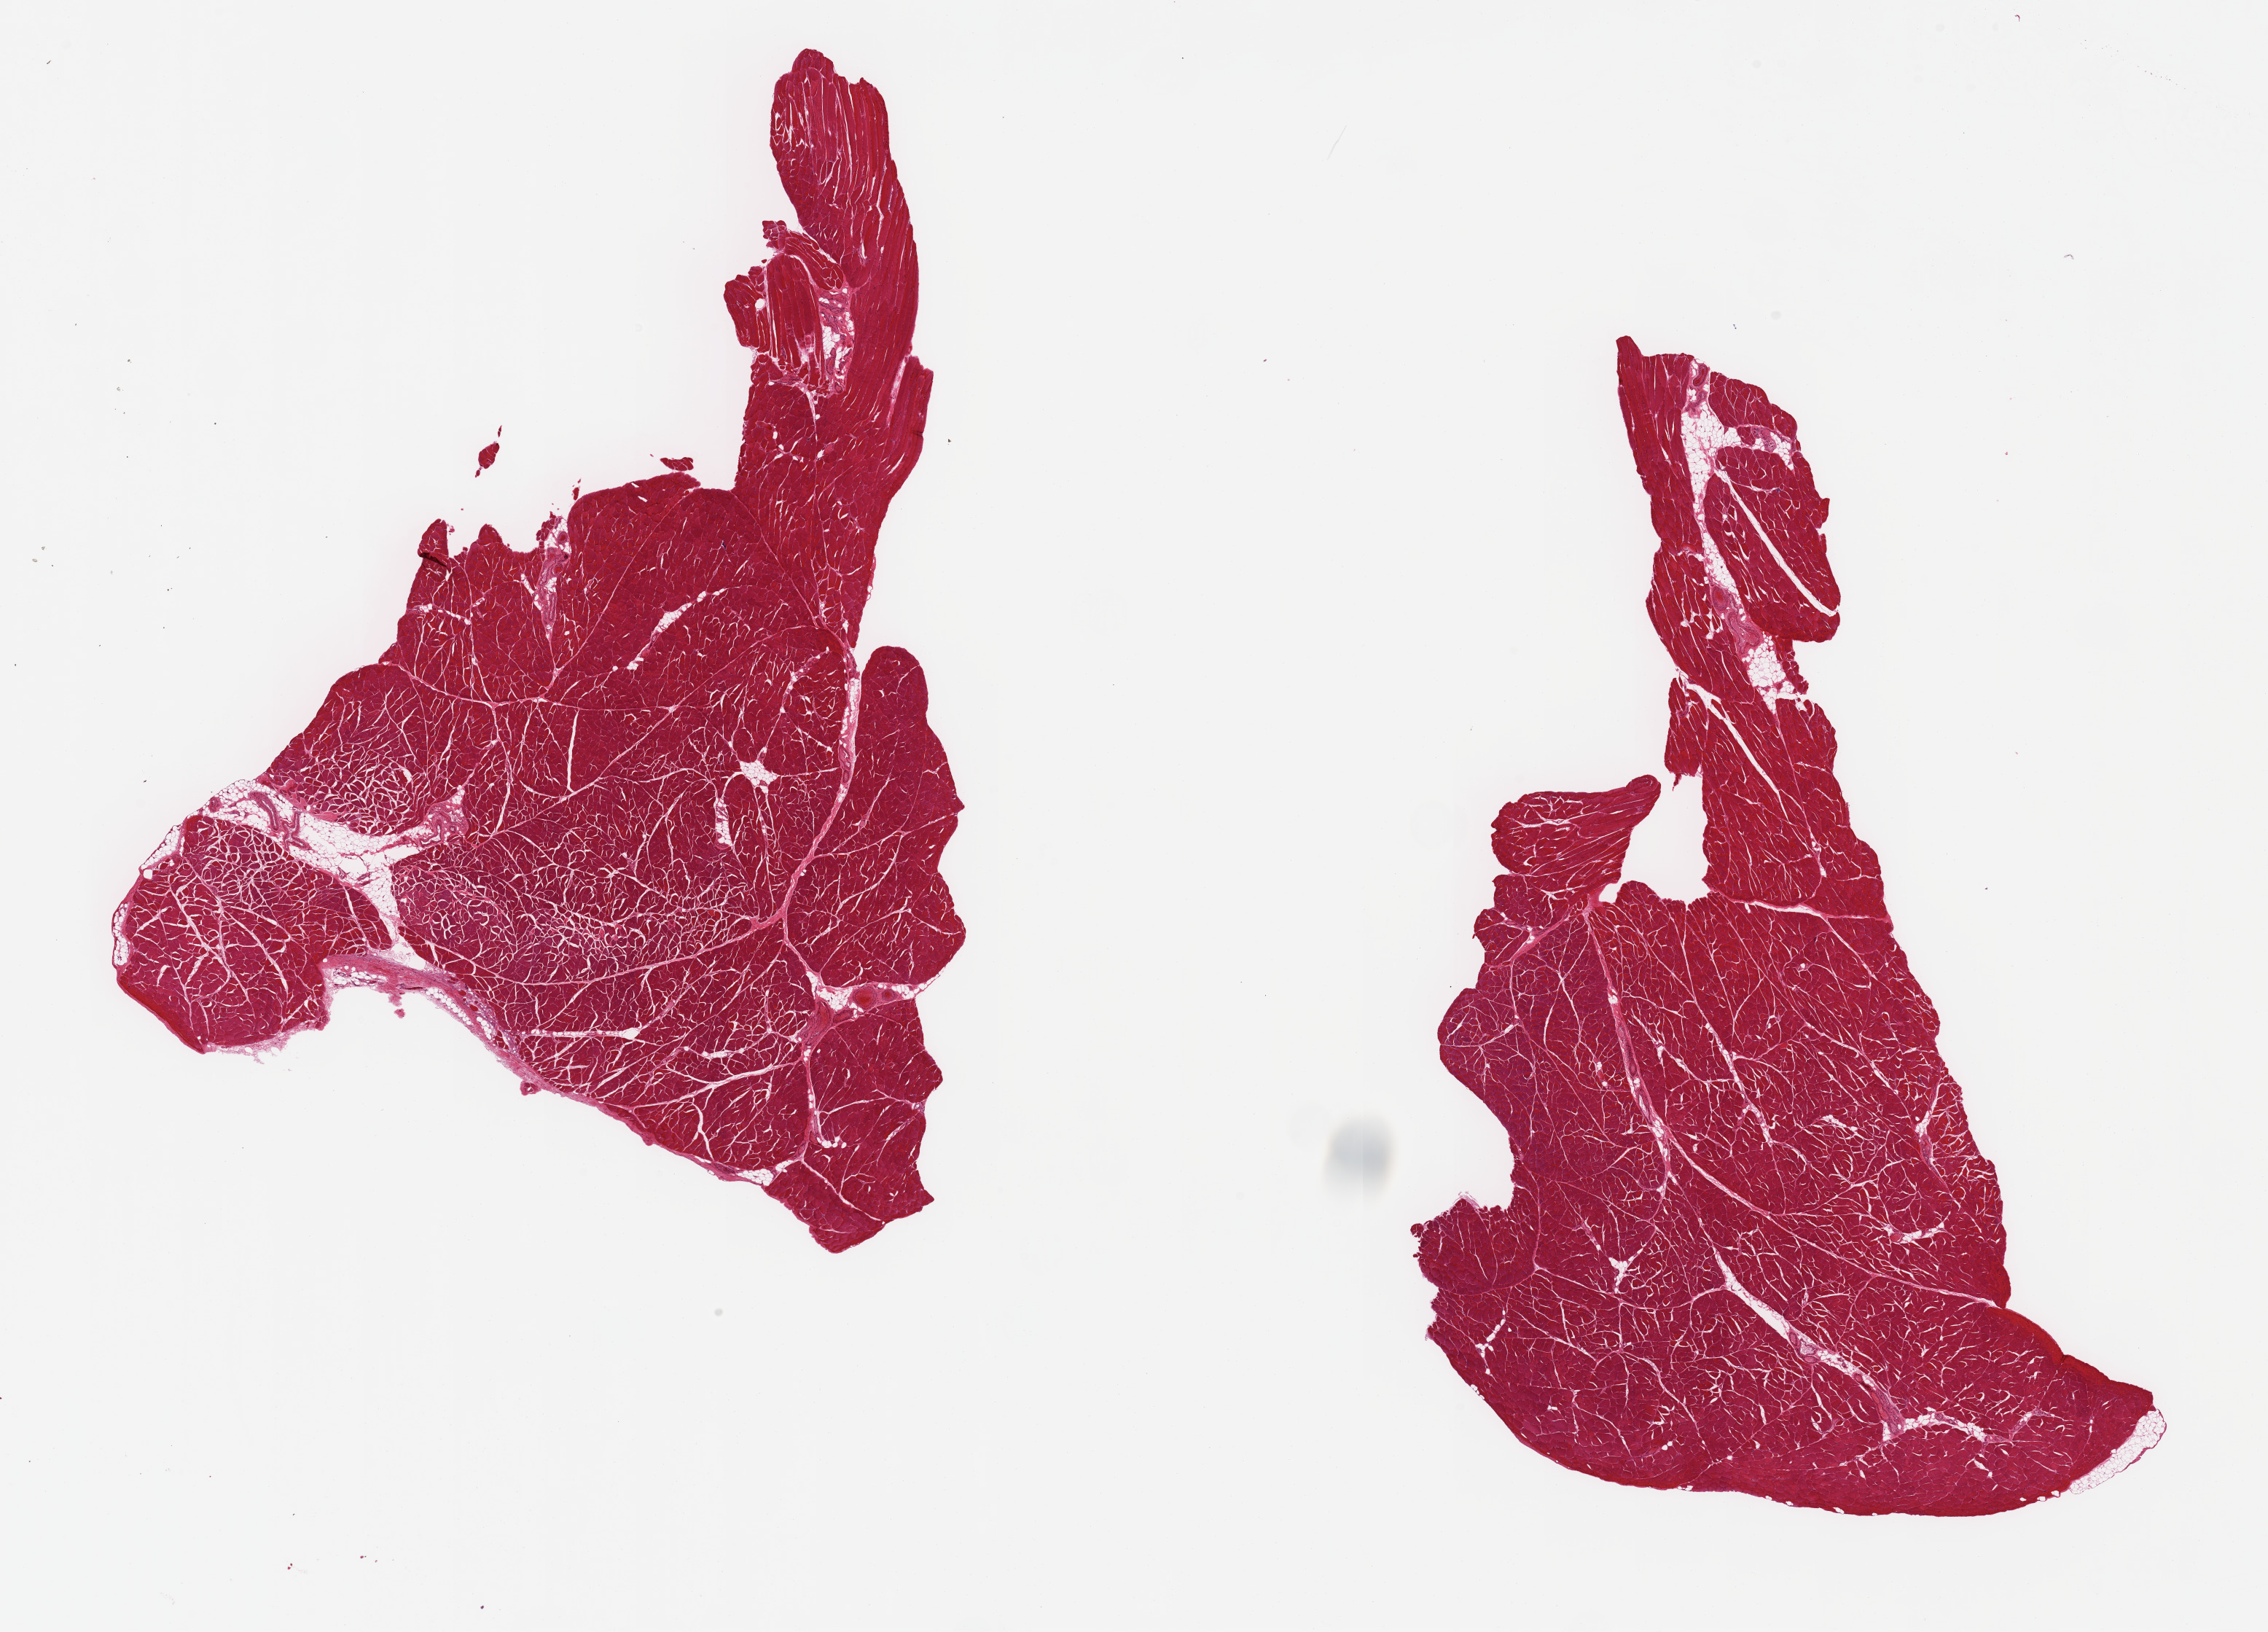
Whole-slide image, haematoxylin and eosin stain, brightfield, shown as a low-resolution overview of the whole scanned area (about 24.6 x 17.7 mm, from a 20x scan), PAXgene-fixed, paraffin-embedded tissue, target tissue: skeletal muscle, tissue donor sample. Male donor.
Pathologist's review note for this sample: 2 pieces, ~5% interstitial fat.